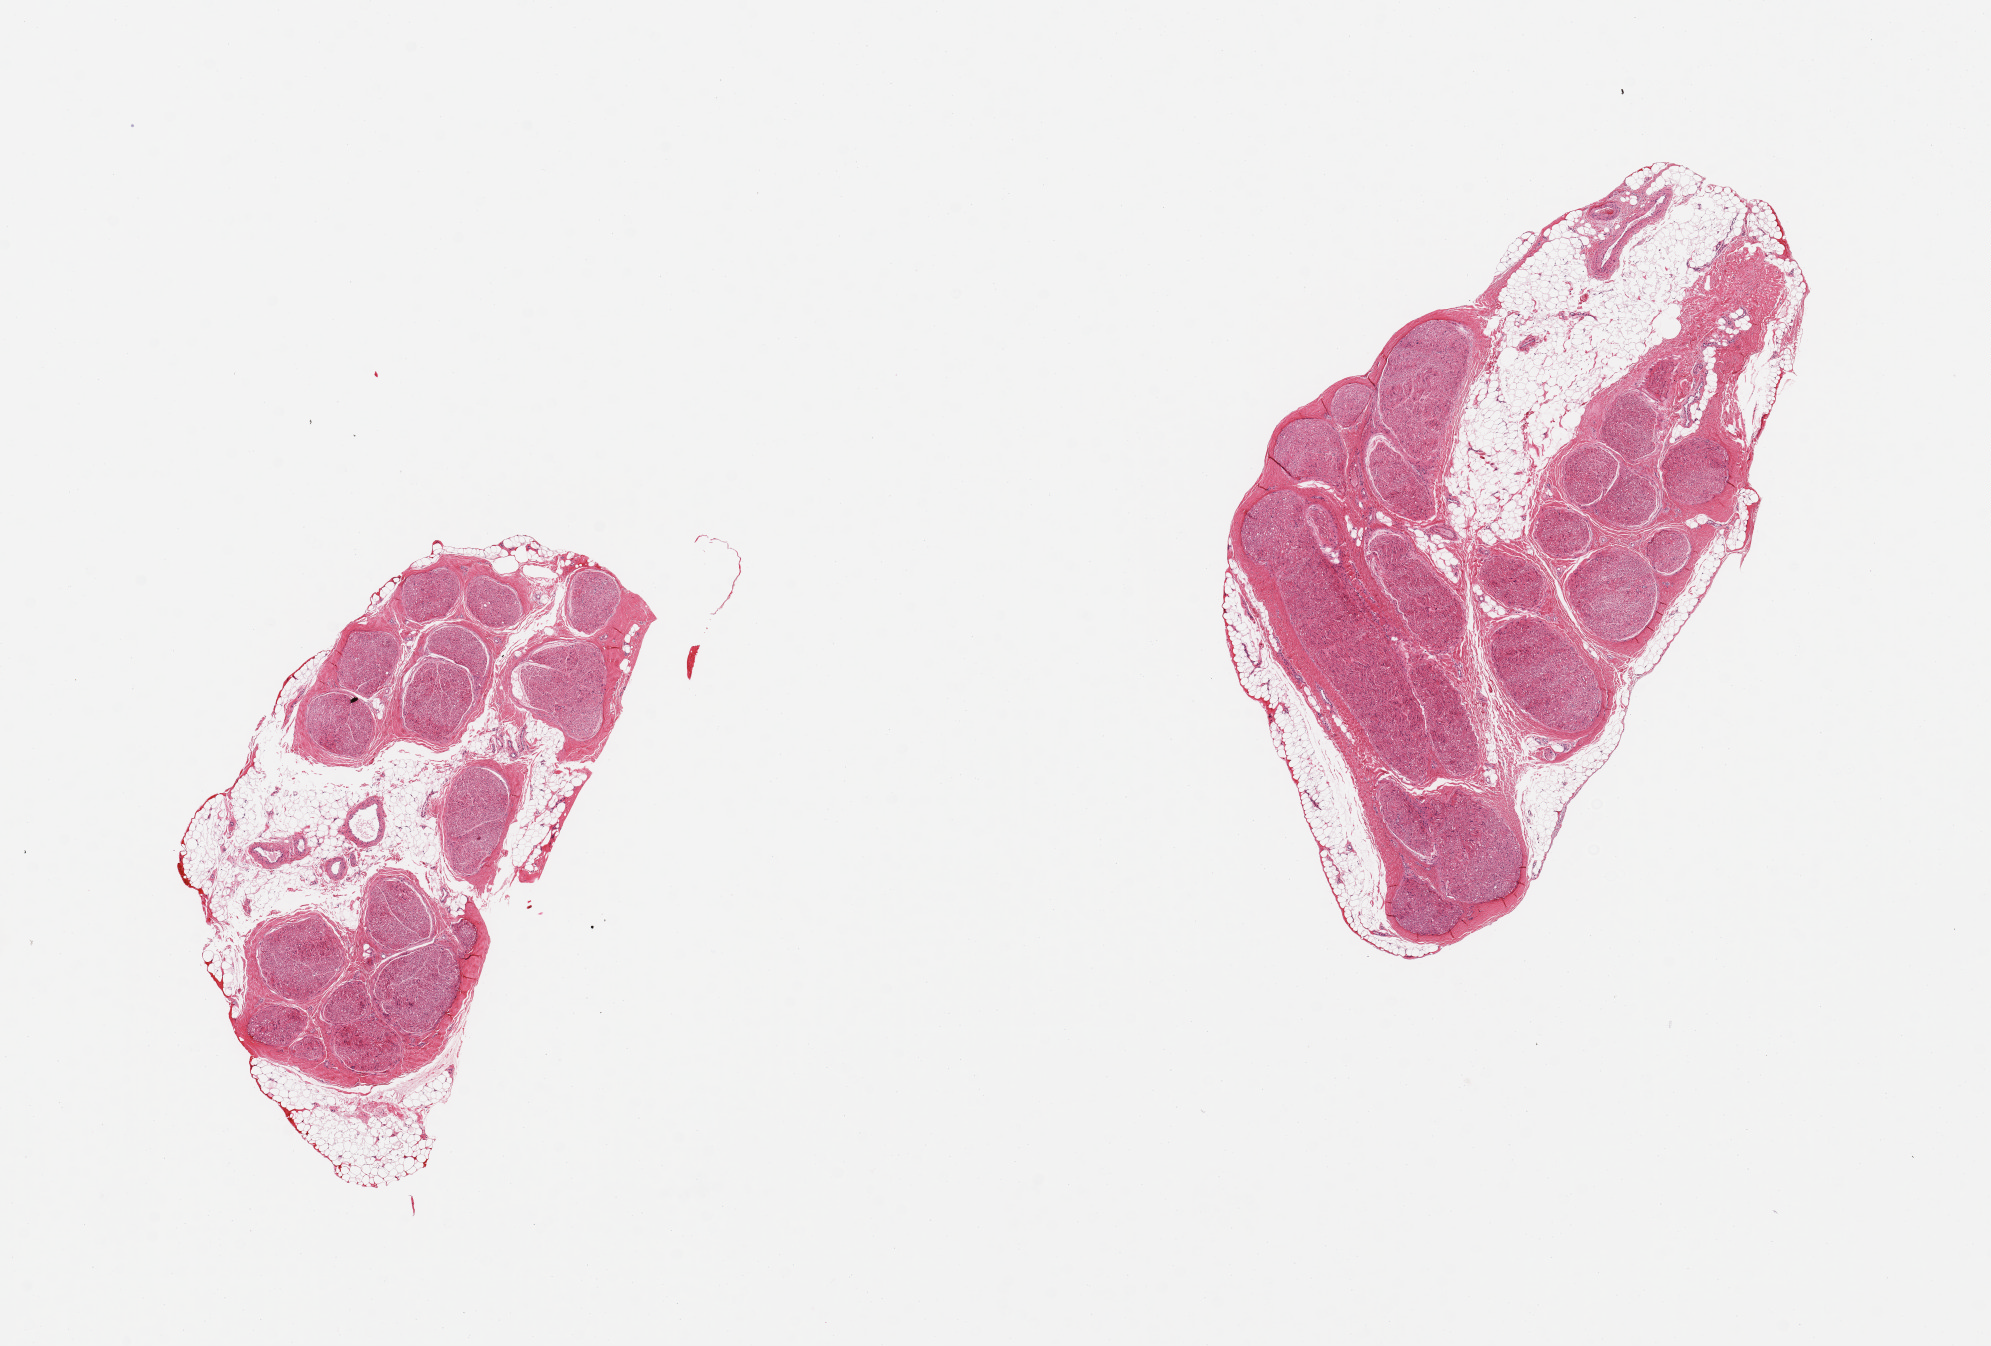
Whole-slide image, H&E stain, brightfield — whole scanned area (about 15.8 x 10.6 mm, from a 20x scan) shown as a low-resolution overview, PAXgene-fixed paraffin-embedded (PFPE) section, sampled site (target tissue): tibial nerve, tissue donor sample. Donor sex: male.
Reviewer comment on this tissue sample: 2 pieces; ~40% internal/external fat.